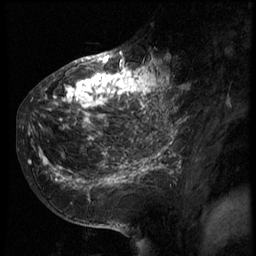
Breast MRI (dynamic contrast-enhanced), one sagittal slice; position 29 of 66 along the scan axis; 3 images stored at this slice position (order not interpretable as contrast timing); 1.5 T; TE 4.2 ms, TR 8.9 ms; 2.5 mm slice thickness; 256 × 256 image matrix, field of view 200 × 200 mm. Patient: female, 39 years. Case-level facts recorded for this patient, not image findings: setting: breast cancer imaged before/during neoadjuvant chemotherapy; receptor status: HER2-positive.
Annotated regions visible in this slice (semi-automatically segmented with operator editing):
- analysis volume of interest (the breast-tissue region the enhancement analysis was run in; not a lesion): bounding box (x1, y1, x2, y2) in pixels: (29, 44, 166, 196)
- tumour enhancement mask (voxels above the 140 % enhancement threshold inside the analysis volume of interest): (29, 57, 166, 188)